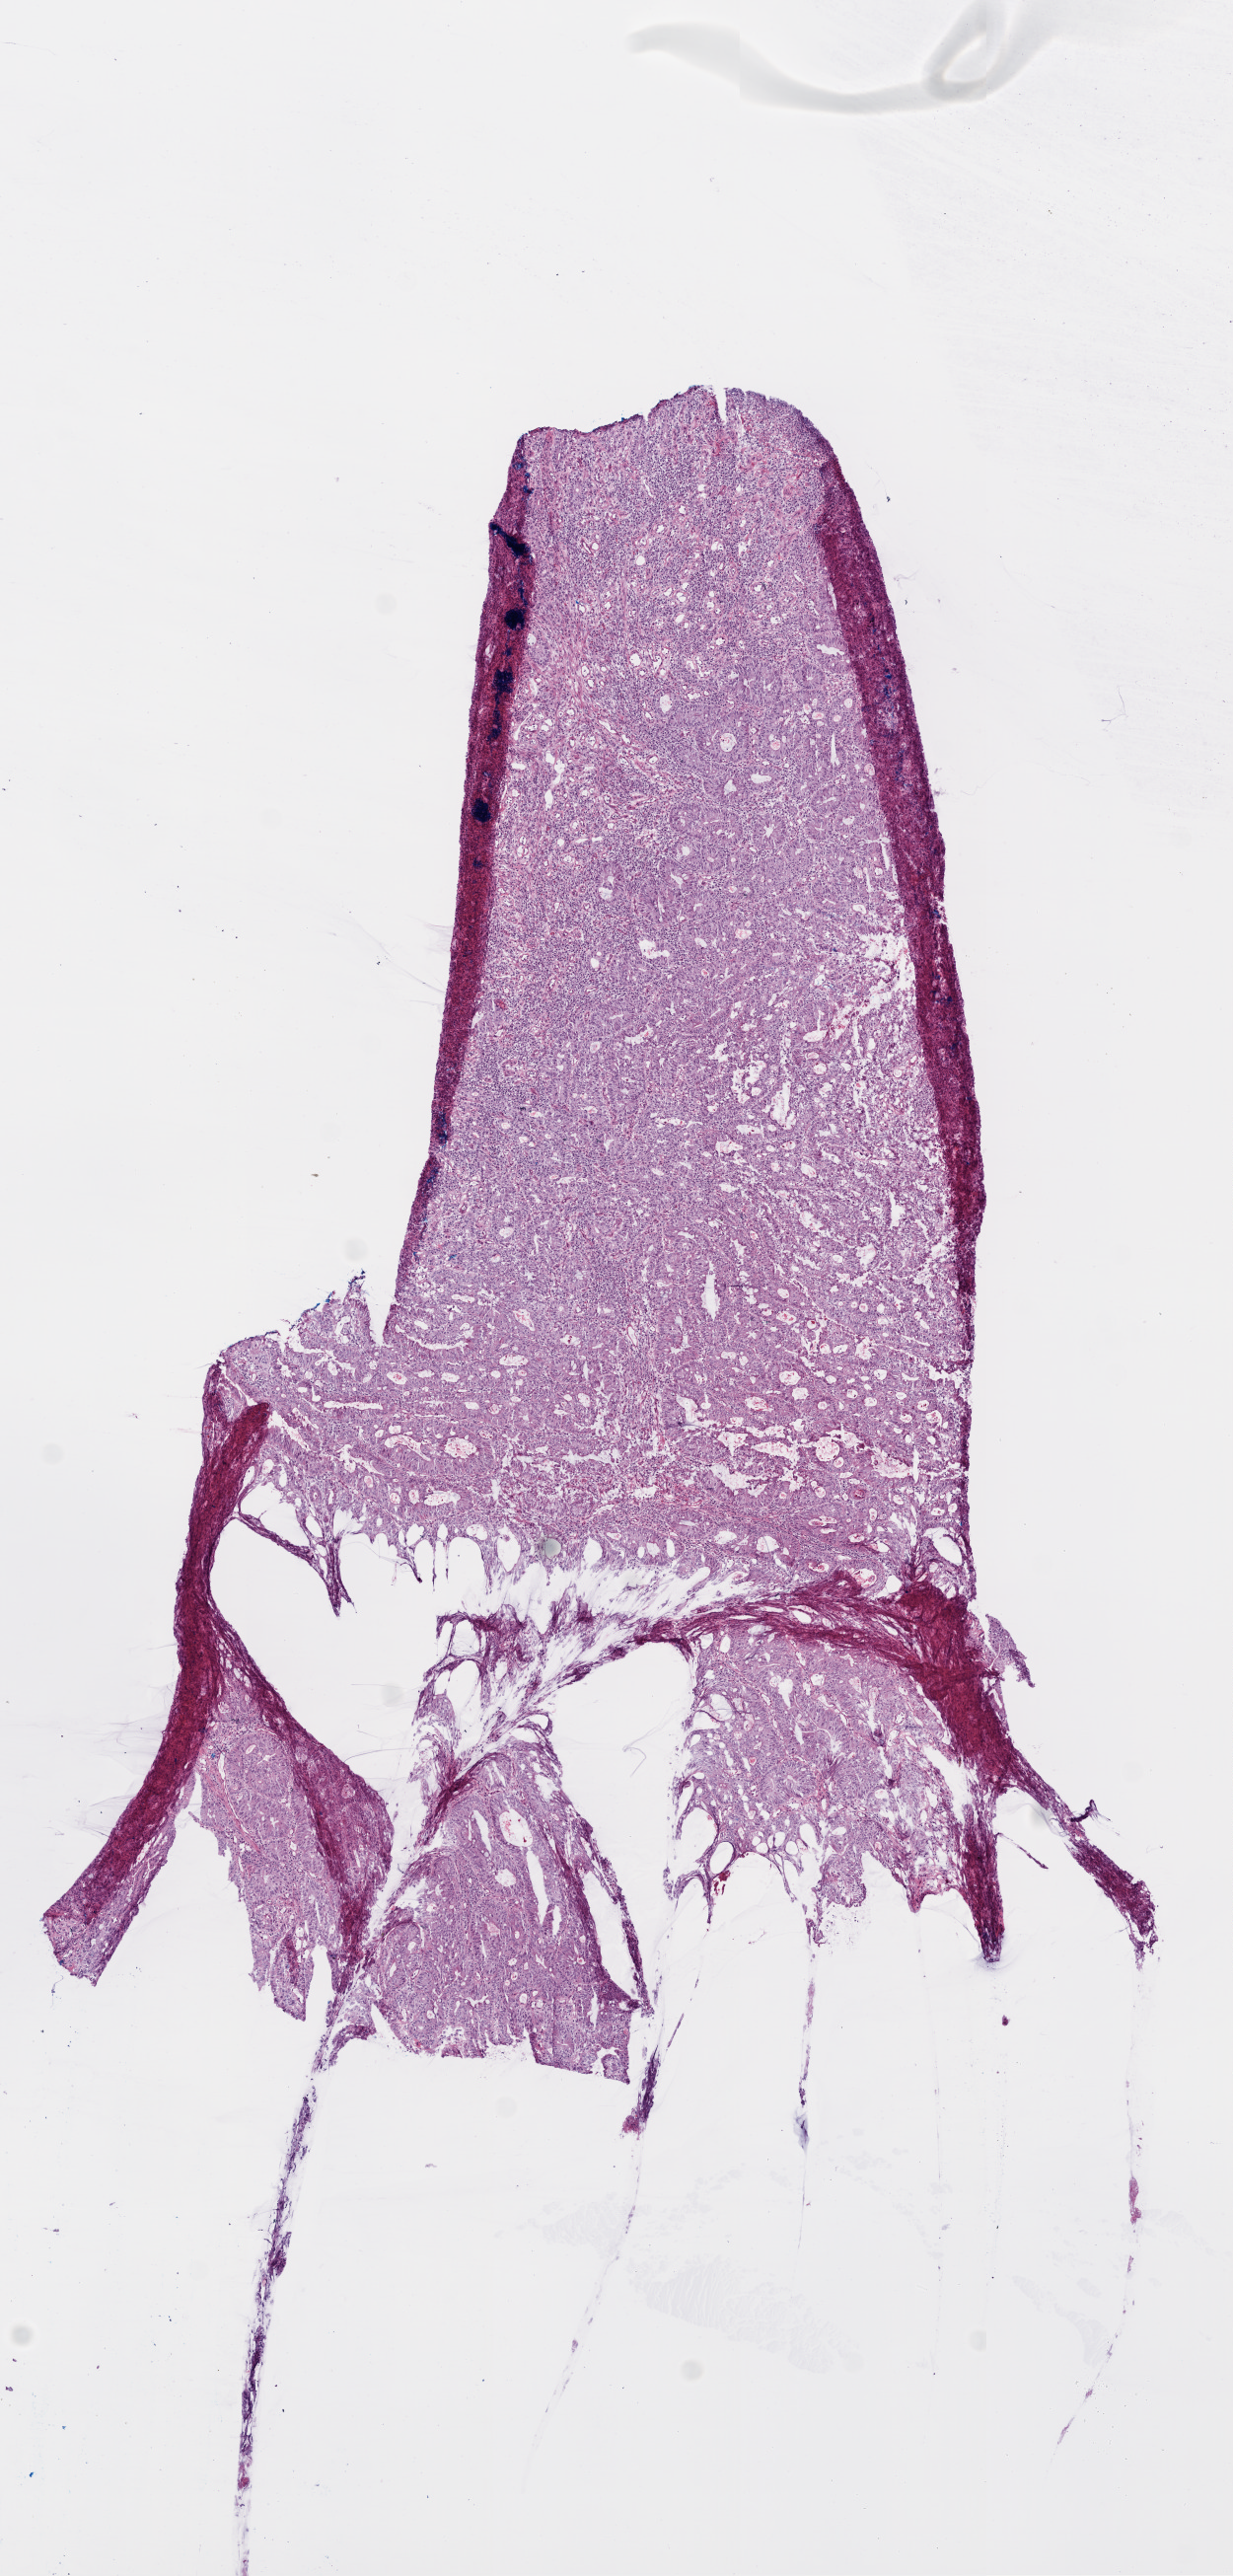
Whole-slide histology image, Hematoxylin and eosin (H&E) stained — whole scanned area (about 5.0 x 10.5 mm, acquisition: 20x scan) shown as a low-resolution overview; frozen section from the top of the tissue portion; colon, primary tumour sample. Male, age 74 years at initial diagnosis. Slide review estimates, as recorded: tumour cells 87%, tumour nuclei 85%, normal cells 0%, stromal cells 5%, necrosis 8%.
* AJCC pathologic stage: I (6th edition)
* TNM: T2 N0 M0
* pathologic diagnosis: Adenocarcinoma, NOS (transverse colon)
* lymph nodes positive (case pathology): 0 of 15 examined